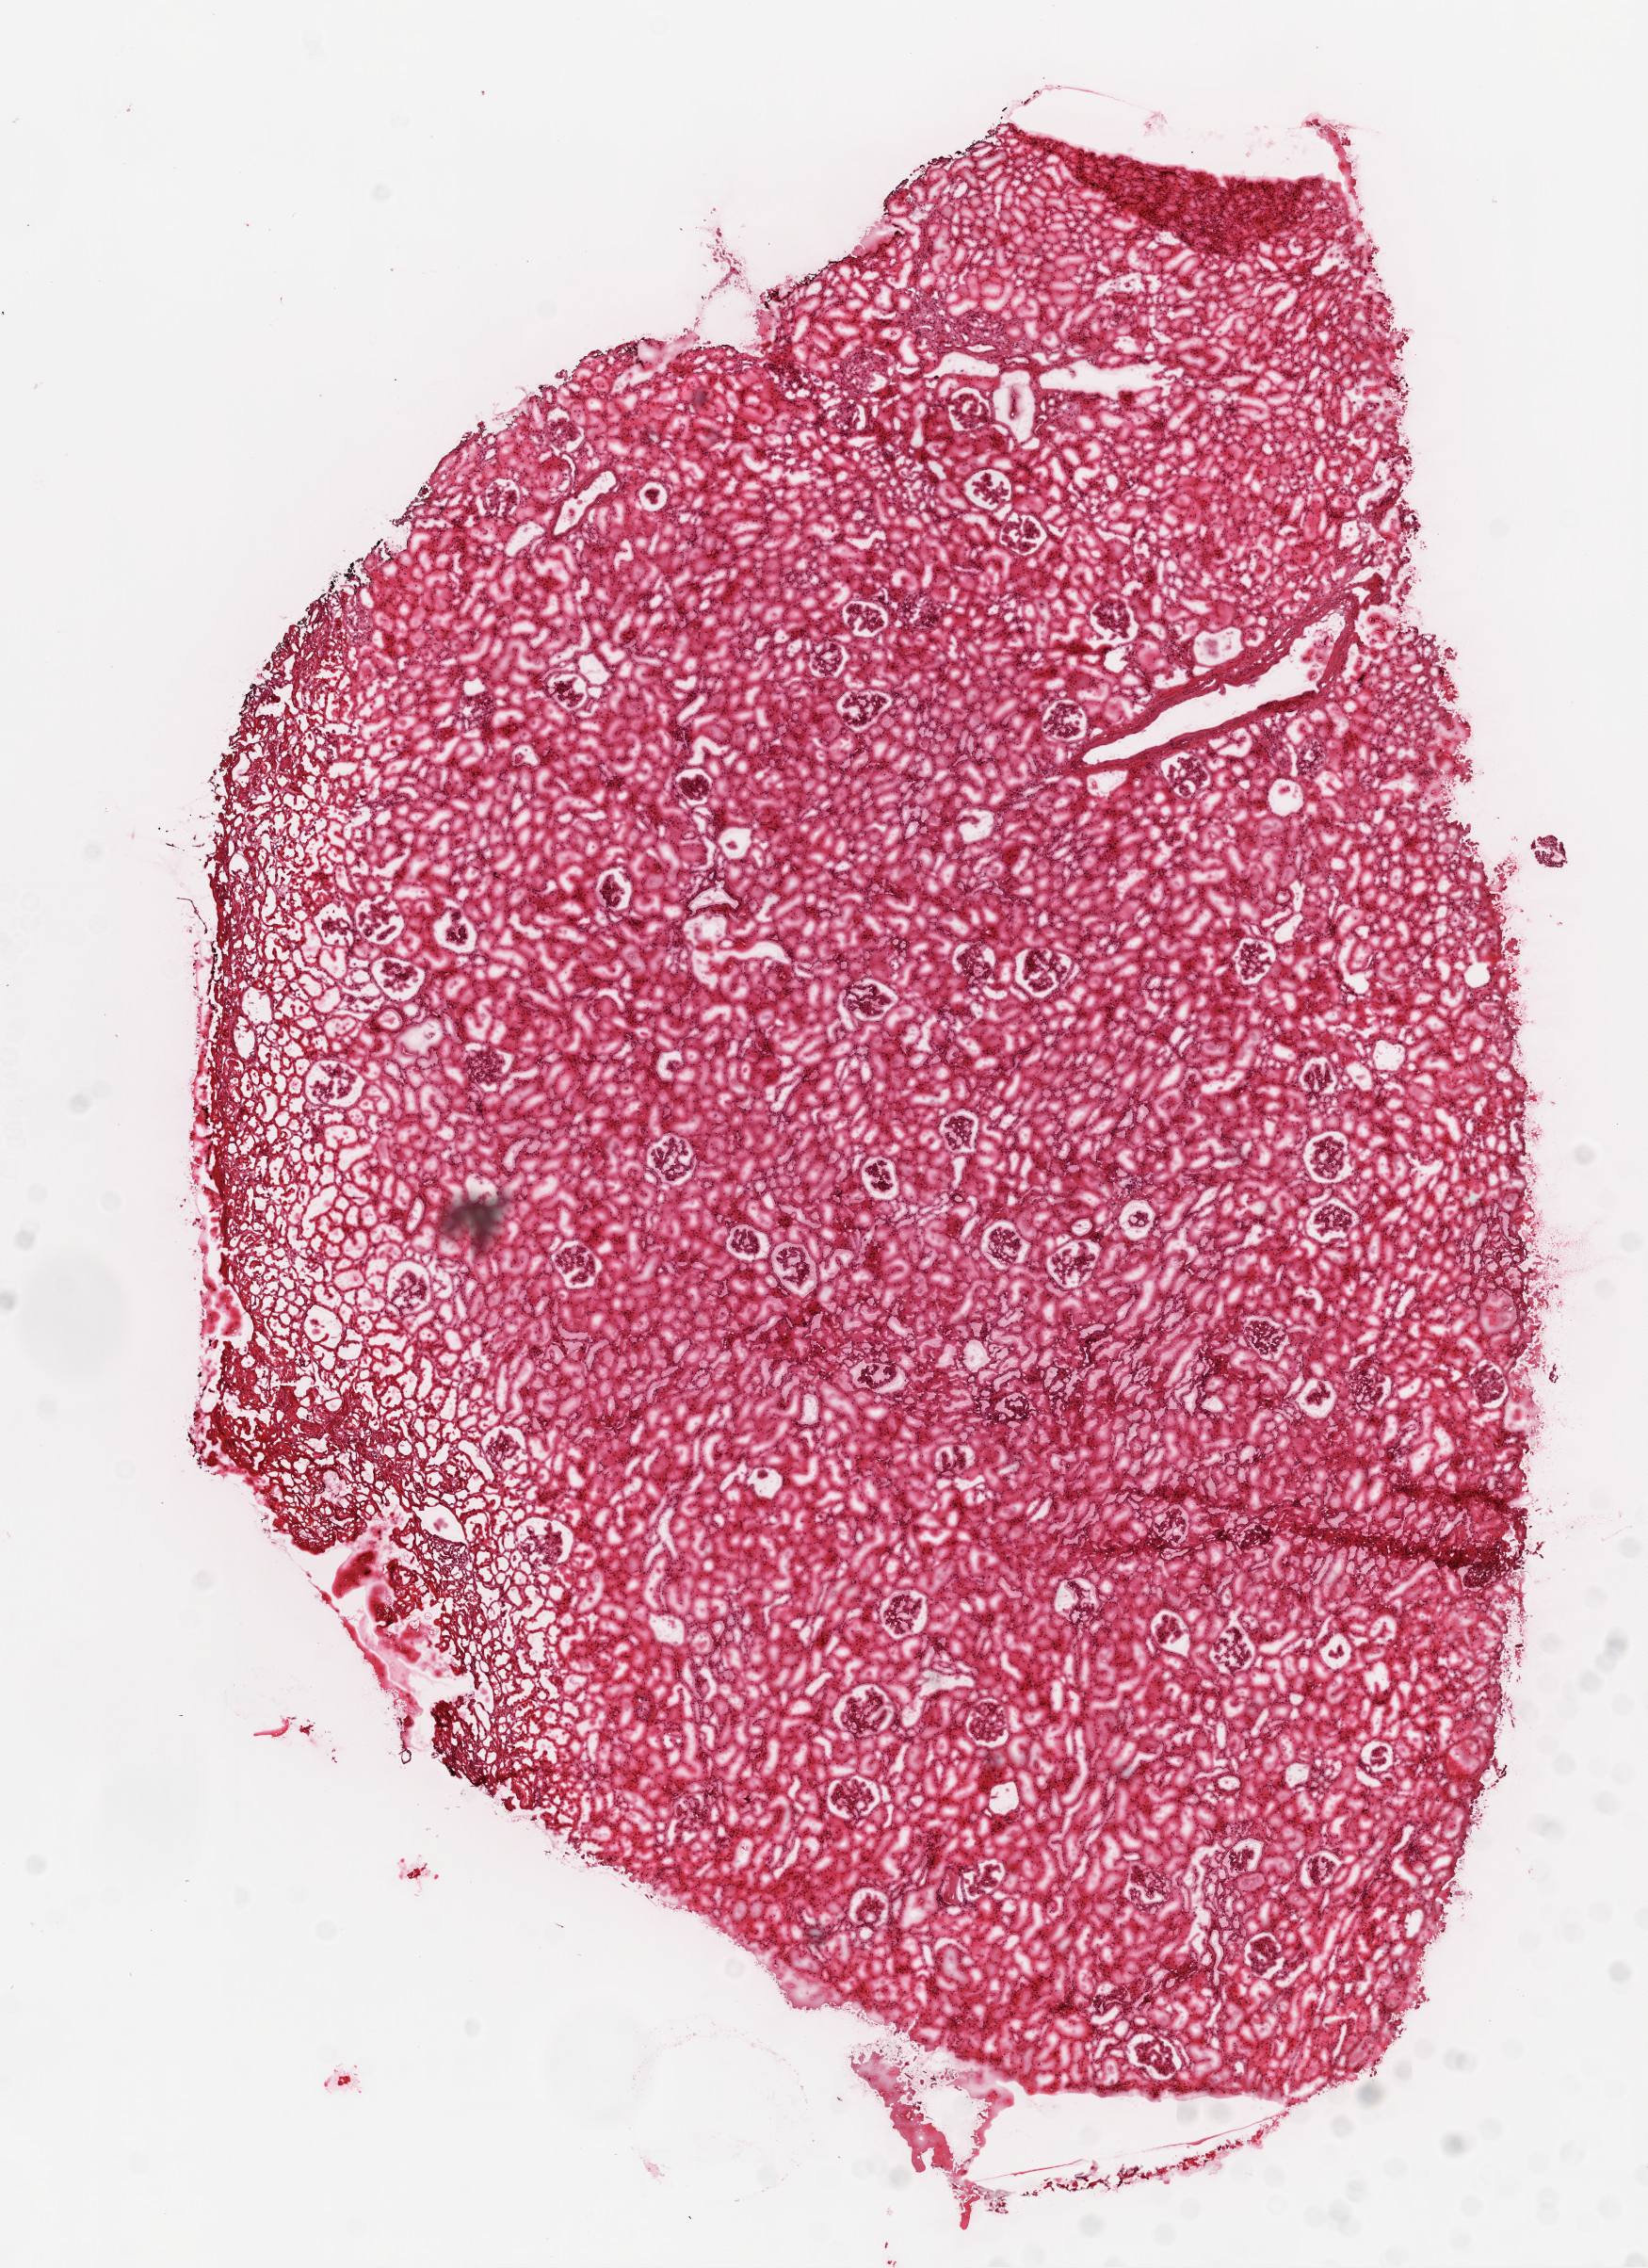
Hematoxylin and eosin (H&E) stained whole-slide image, low-resolution overview of the scanned area, about 7.0 x 9.7 mm; frozen section from the top of the tissue portion; kidney, solid tissue normal (non-tumour tissue) sample. Patient: male, age at initial diagnosis 46 years.
• this section: solid tissue normal sample (biorepository sample class)
• patient diagnosis: Clear cell adenocarcinoma, NOS